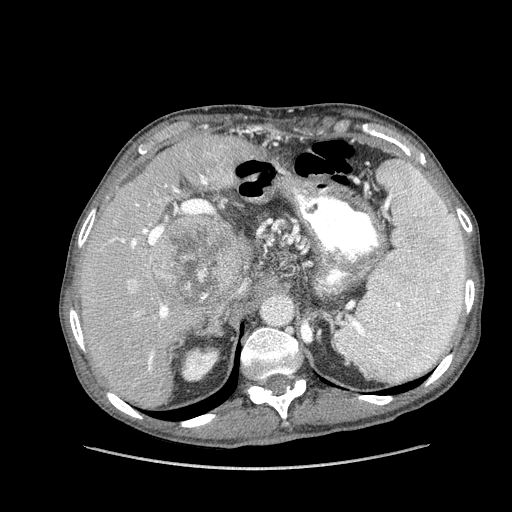
Contrast-enhanced abdominal CT (liver protocol), one axial slice. Reconstruction kernel STANDARD. 100 kVp. Soft-tissue window (W 400 / L 40 HU). 2.5 mm slice thickness. 512 × 512 image matrix, field of view 400 × 400 mm. From the clinical record (not read from this slice): diagnosis: hepatocellular carcinoma (patient treated with transarterial chemoembolisation; whether this scan precedes or follows treatment is not stated here); TNM stage (as recorded): Stage-IIIA; Child-Pugh class: A.
Annotated regions visible in this slice (semi-automatically segmented with operator editing):
- liver parenchyma outside the tumour (the mass and vessels are separate outlines, so this box may not span the whole liver): box from (x=80, y=134) to (x=257, y=408) px
- mass: (x=151, y=212)–(x=248, y=310)
- liver vessels: (x=109, y=146)–(x=230, y=371)